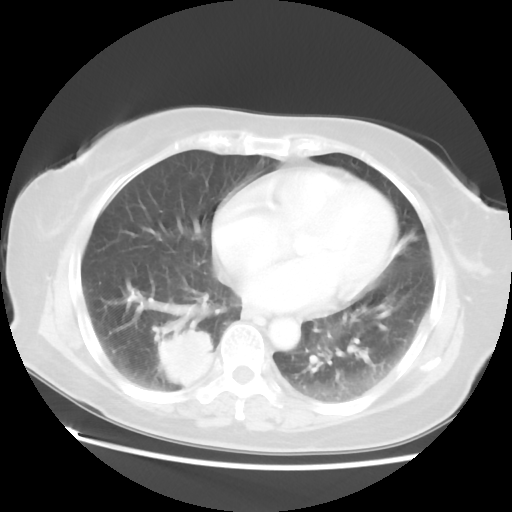
Chest CT, one axial slice. Position 23 of 52 along the scan axis. Reconstruction kernel STANDARD. Lung window (W 1500 / L -600 HU). 5 mm slice thickness. 512 × 512 image matrix, field of view 356 × 356 mm. Patient: female, 69 years. Case-level facts recorded for this patient, not image findings: clinical TNM (as recorded): T2 N1 M1a.
Annotated regions visible in this slice (bounding box drawn by a radiologist):
- lung tumour (recorded histology: adenocarcinoma): bounding box [x1, y1, x2, y2] px = [146, 324, 219, 392]